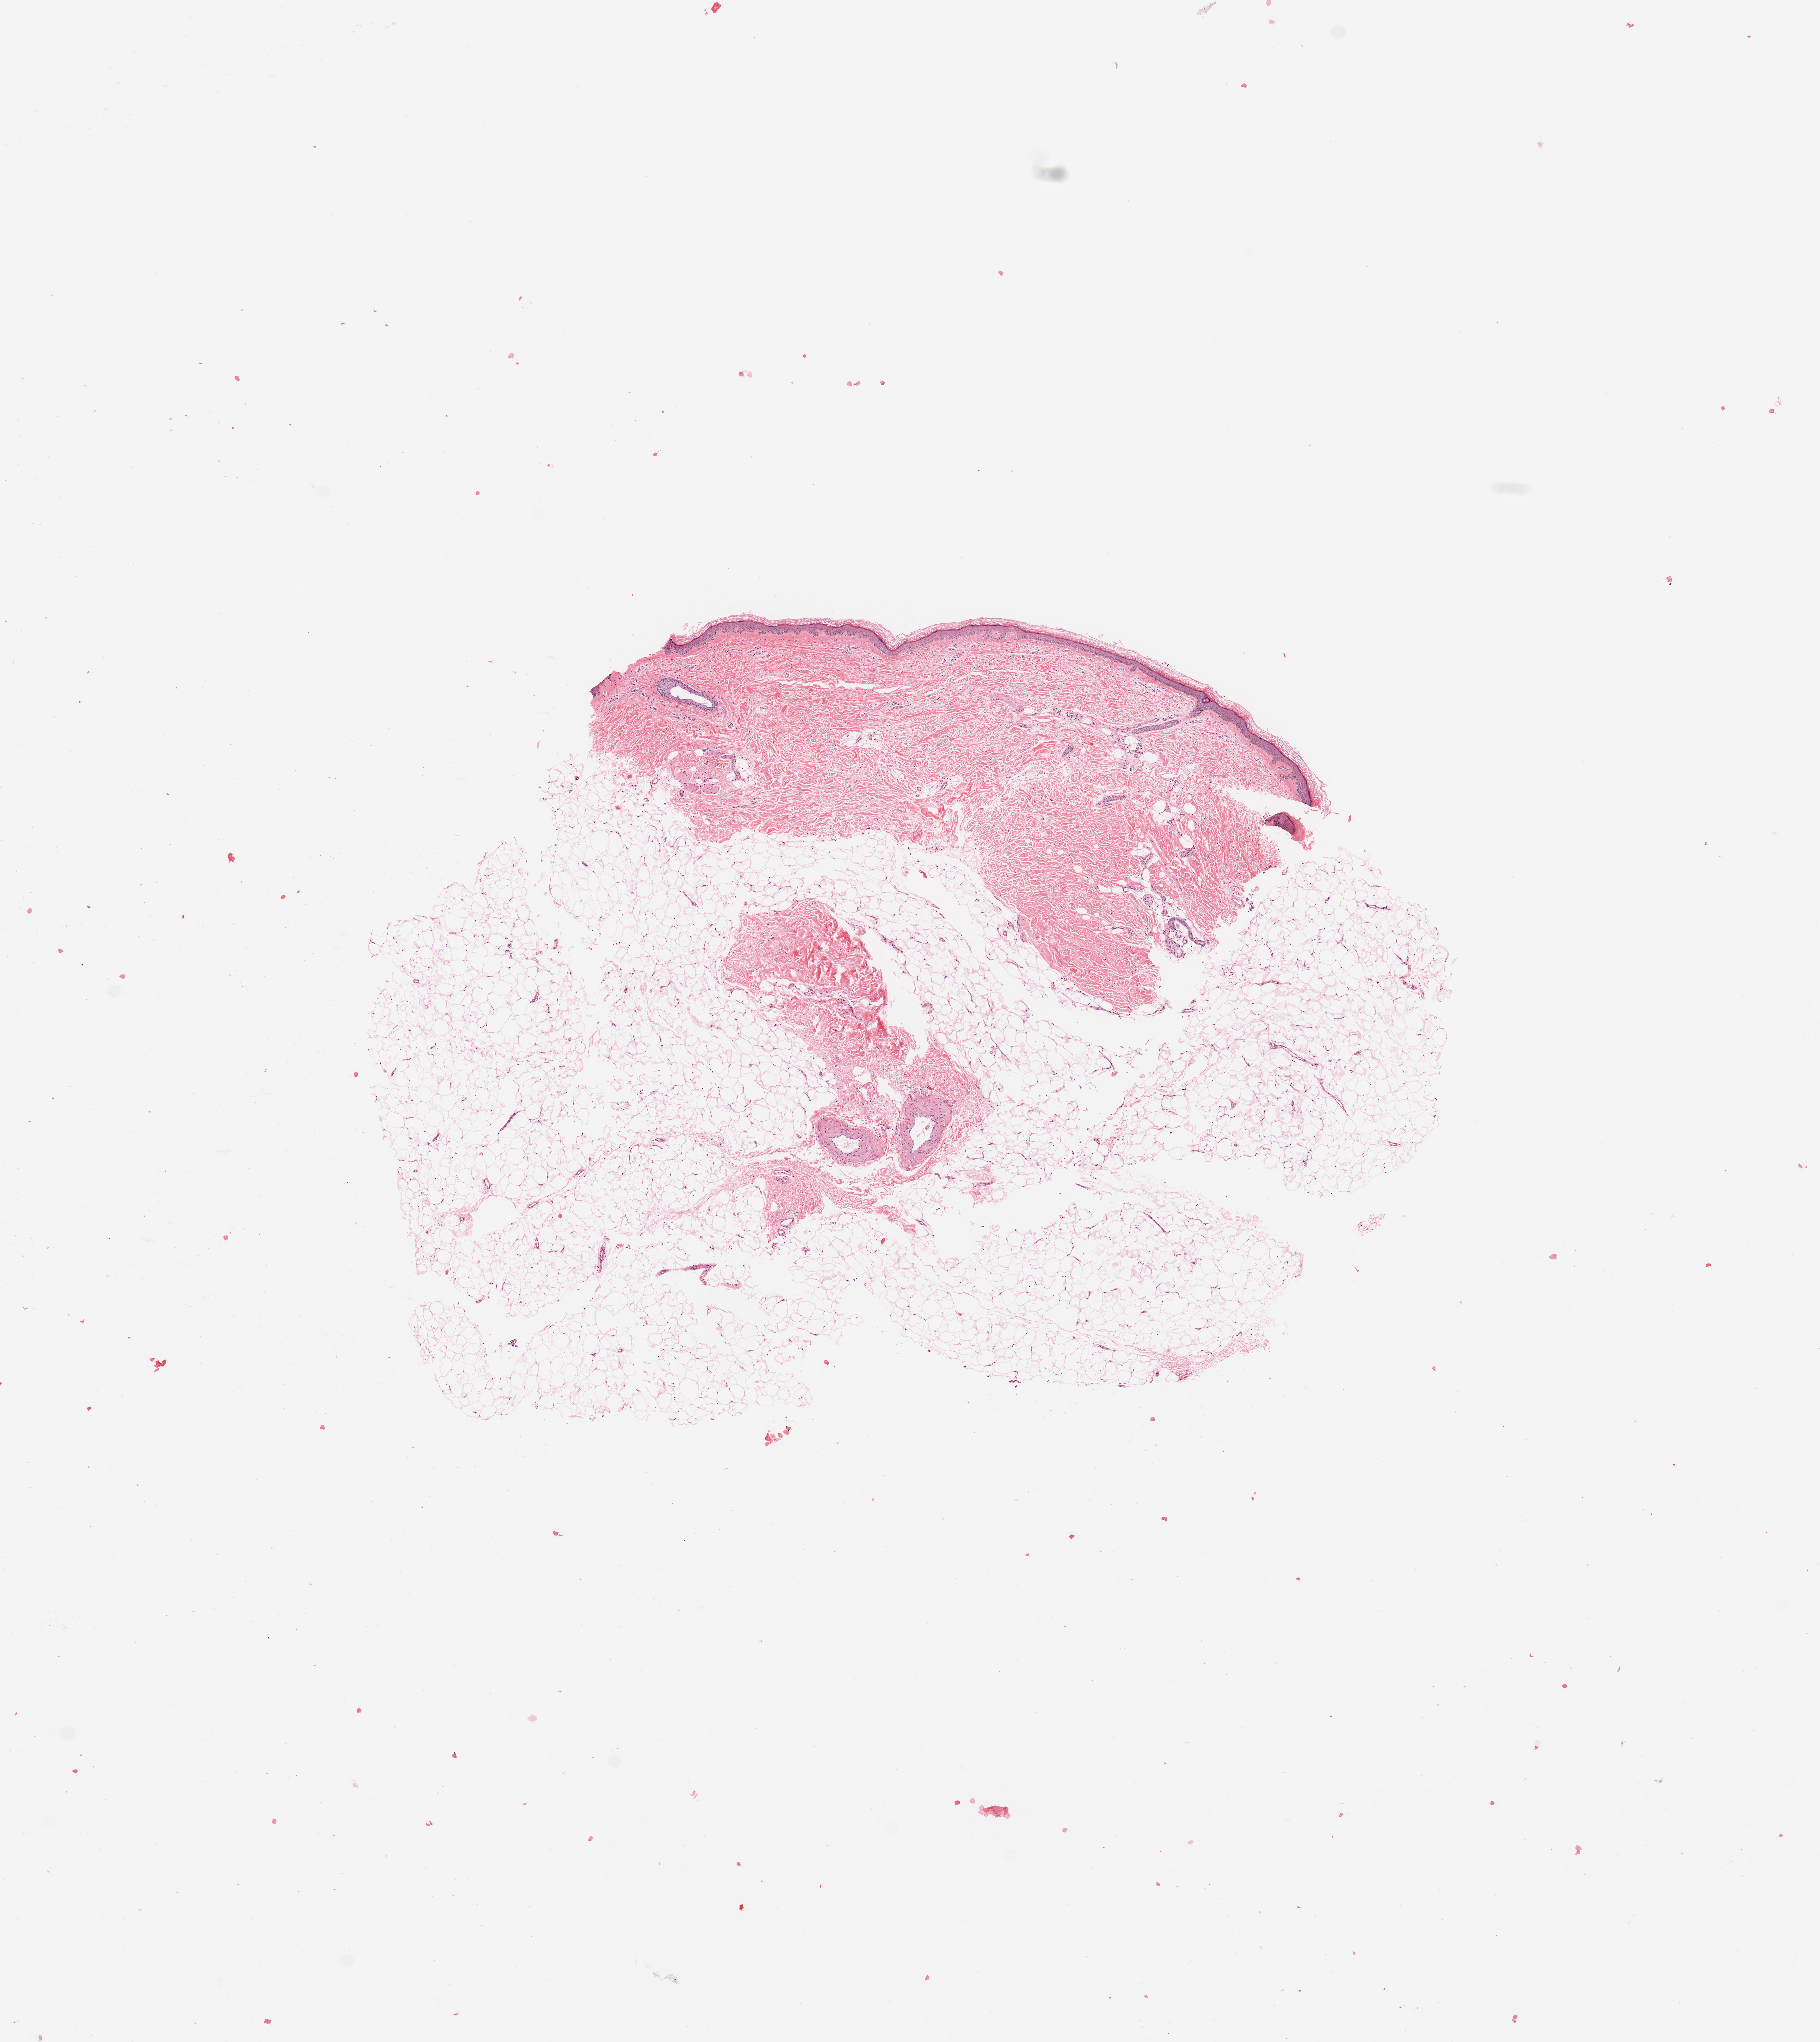
Digitized H&E-stained tissue section (whole slide), whole scanned area (about 10.8 x 12.1 mm, slide scanned at 20x) shown as a low-resolution overview, normal (non-tumour) tissue (melanoma cohort); sampled site not recorded. Female, 64 y/o.
This section: normal (non-tumour) tissue from the same patient. Patient diagnosis: Malignant melanoma, NOS.